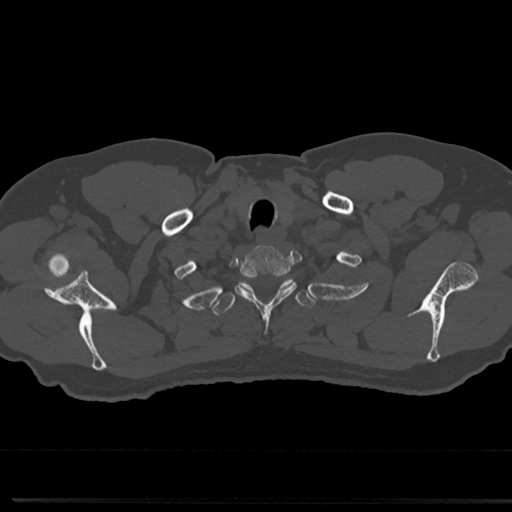
CT including the spine, one axial slice. Slice 659 of 817 in the series (ordered by position). 120 kVp. Bone window (W 1800 / L 400 HU). 0.5 mm slice thickness. 512 × 512 image matrix. Patient: male, 61 years. Case-level facts recorded for this patient, not image findings: primary cancer: prostate.
Structures marked on this image (semi-automatic segmentation, software-assisted and operator-edited):
- T1 vertebra: bounding box [x1, y1, x2, y2] px = [237, 248, 294, 302]
- T2 vertebra: [215, 278, 313, 314]